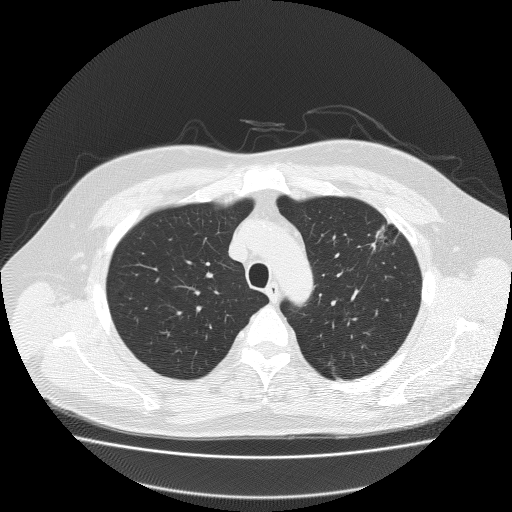
Low-dose screening chest CT, one axial slice; position 158 of 204 along the scan axis; lung window (W 1500 / L -600 HU); 2 mm slice thickness; 512 × 512 image matrix, field of view 410 × 410 mm.
Annotated regions visible in this slice (manually delineated by an expert):
- lesion 1 (tumor, upper lobe of left lung): bounding box [x1, y1, x2, y2] px = [372, 222, 392, 249]